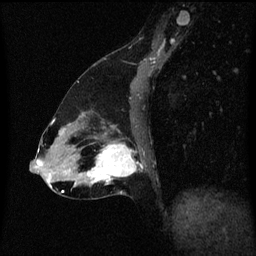
Breast MRI (dynamic contrast-enhanced), one sagittal slice; slice 27 of 60 in the series (ordered by position); dynamic contrast-enhanced series, image 2 of 3 at this slice position (ordered by acquisition); 1.5 T; TE 4.2 ms, TR 8.4 ms; 2 mm slice thickness; 256 × 256 image matrix, field of view 200 × 200 mm. Patient: female, 47 years.
Structures marked on this image (semi-automatically segmented with operator editing):
- analysis volume of interest (the breast-tissue region the enhancement analysis was run in; not a lesion): box from (x=85, y=136) to (x=140, y=195) px
- tumour enhancement mask (voxels above the 70 % enhancement threshold inside the analysis volume of interest): (x=86, y=144)–(x=136, y=185)